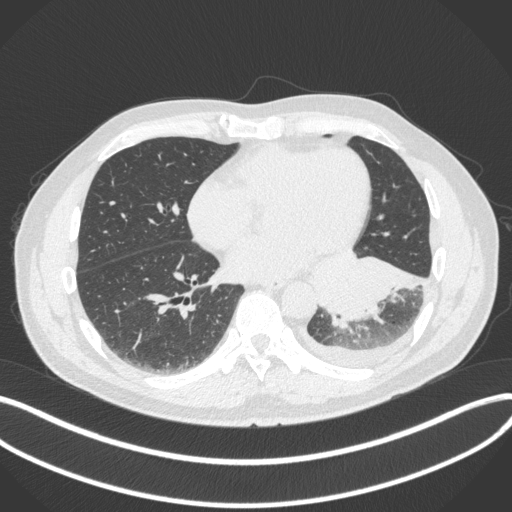
Chest CT, one axial slice; reconstruction kernel B31f; lung window (W 1500 / L -600 HU); 512 × 512 image matrix. Patient: male, 58 years. From the clinical record (not read from this slice): clinical TNM (as recorded): T3 N1 M1b.
Structures marked on this image (bounding box drawn by a radiologist):
- lung tumour (recorded histology: small cell carcinoma): bounding box [x1, y1, x2, y2] px = [314, 252, 426, 336]